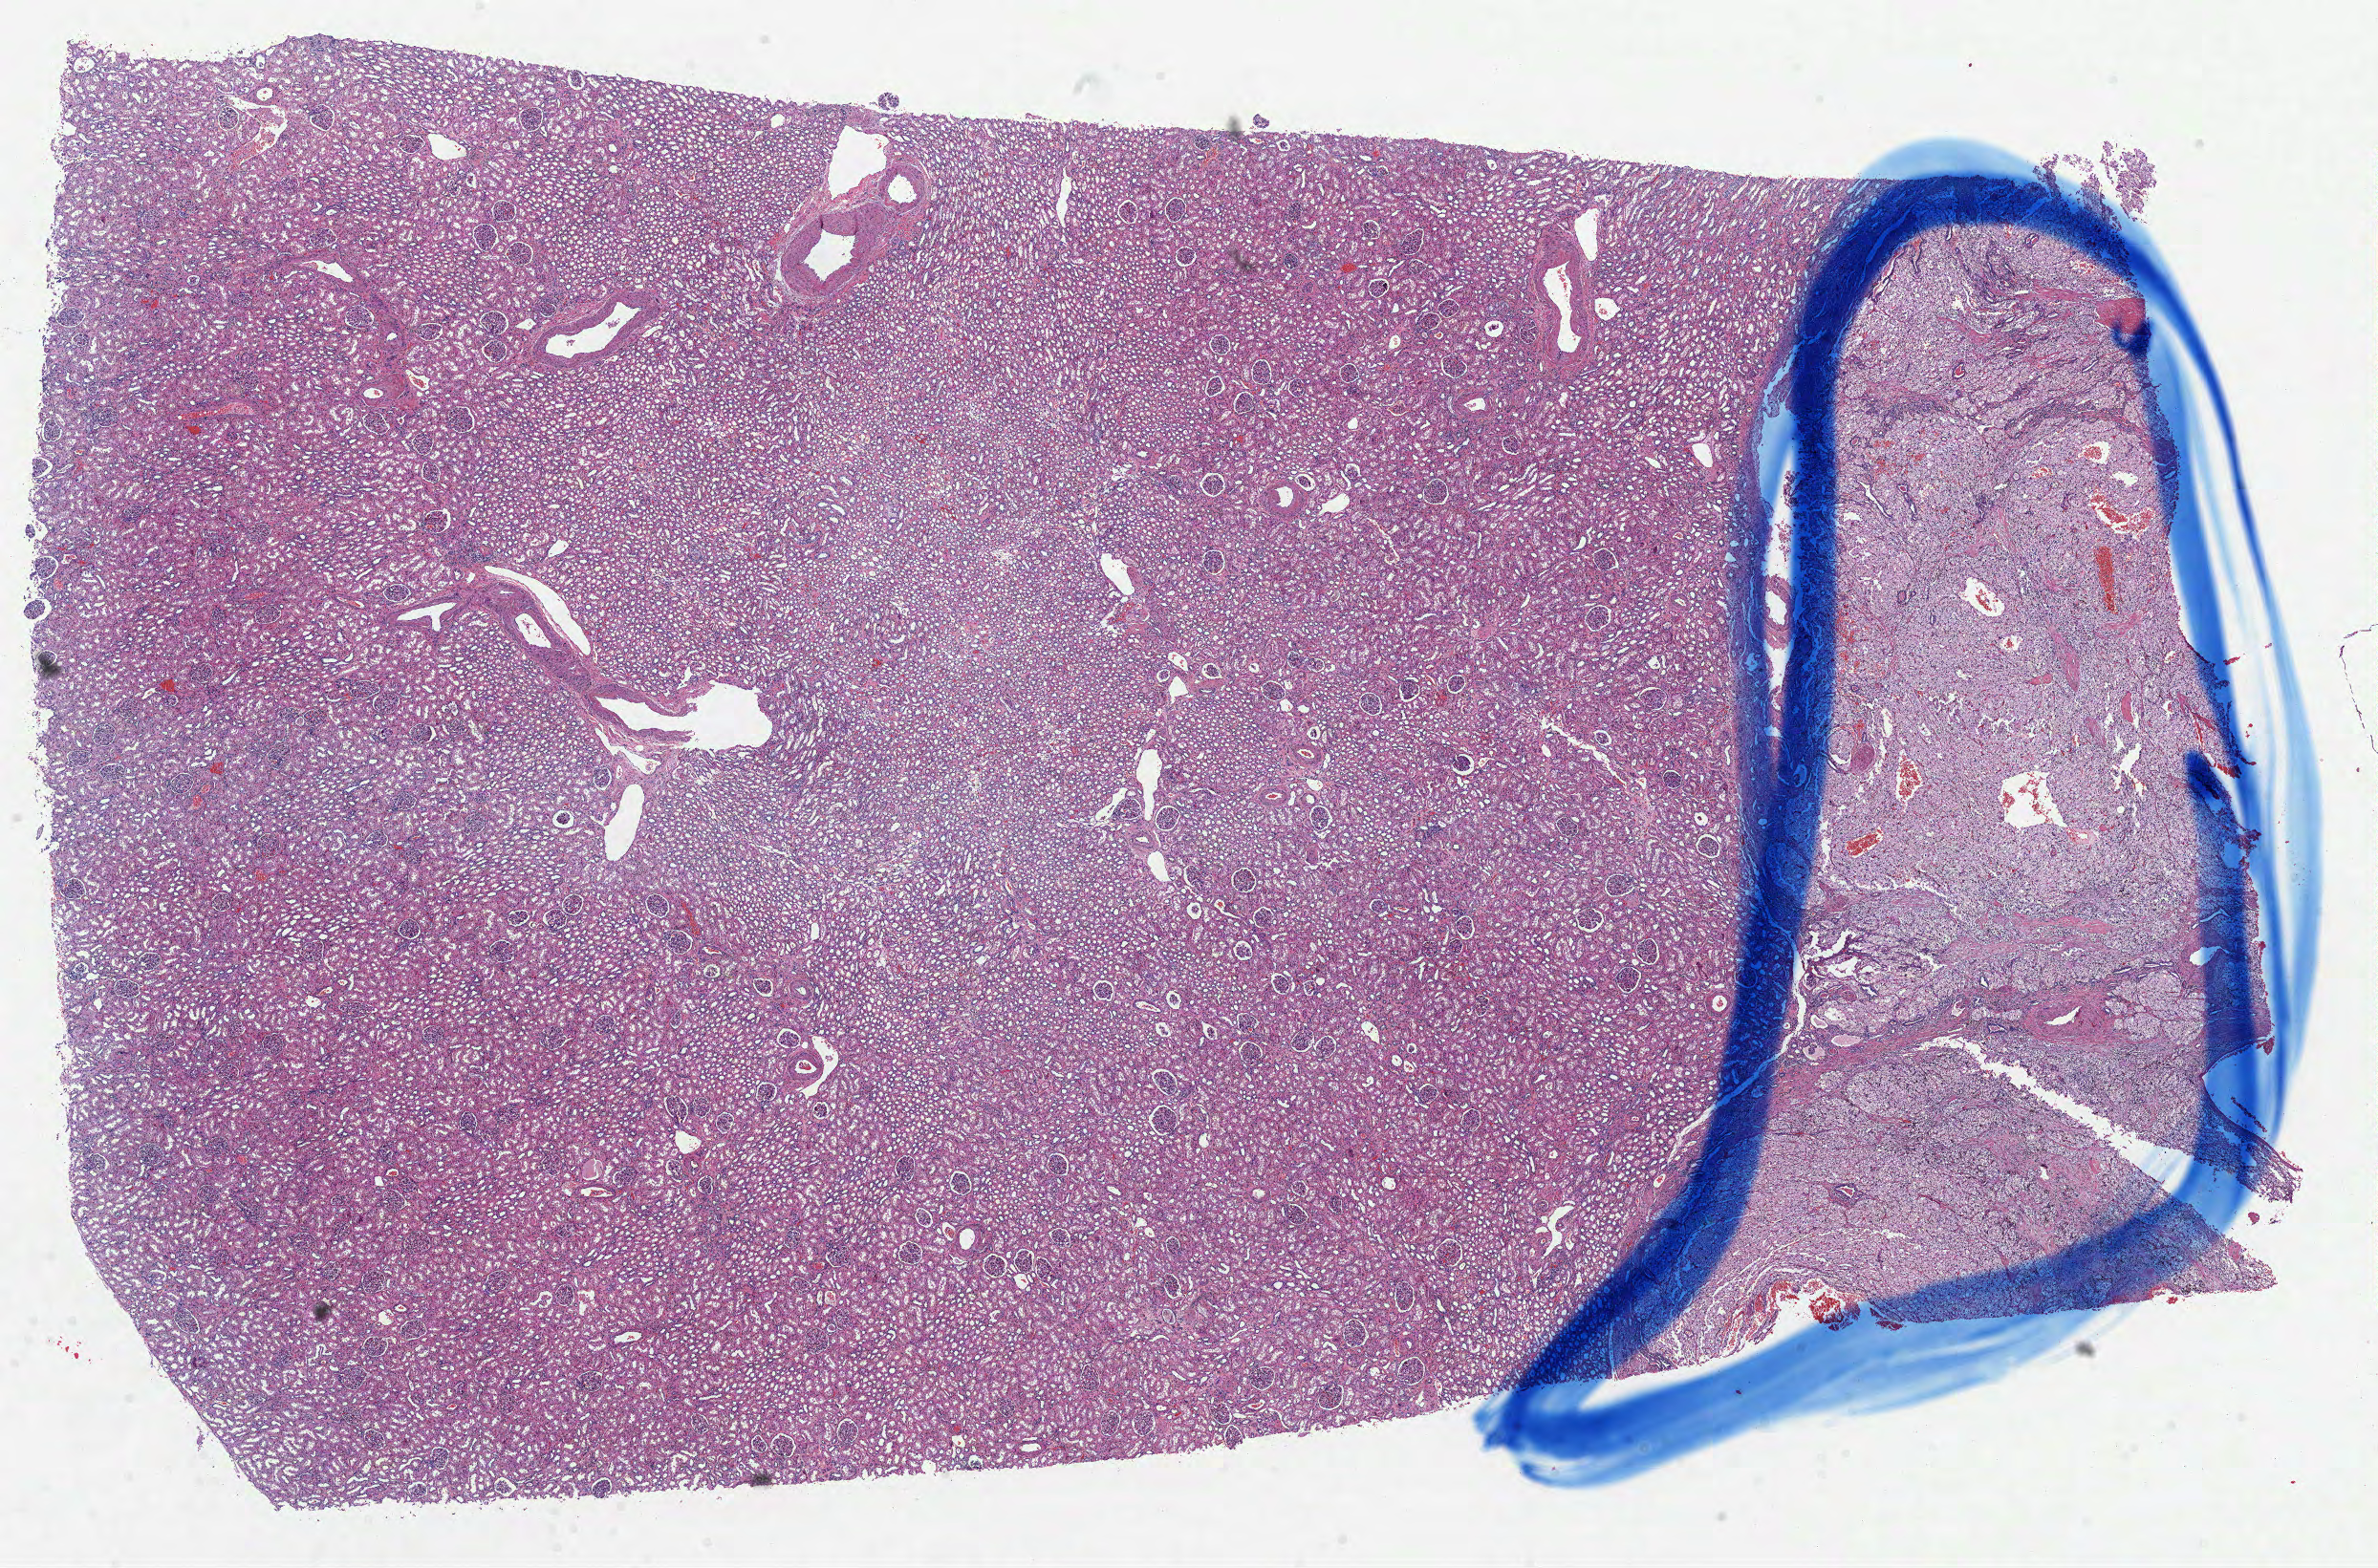
Hematoxylin and eosin (H&E) stained whole-slide image, low-resolution overview of the scanned area, about 20.1 x 13.2 mm (from a 40x scan); formalin-fixed paraffin-embedded (FFPE) diagnostic section; sample: primary tumour, kidney. Patient: male, age at initial diagnosis 63 years. Histologic grade: G3 (poorly differentiated).
* histologic diagnosis: Clear cell adenocarcinoma, NOS
* laterality: left
* AJCC pathologic stage: I